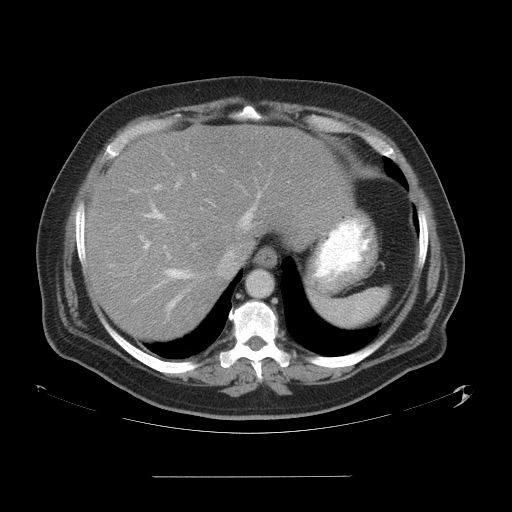
Contrast-enhanced abdominal CT, one axial slice; slice 44 of 58 in the series (ordered by position); 120 kVp; intravenous contrast given; soft-tissue window (W 400 / L 40 HU); 5 mm slice thickness; 512 × 512 image matrix, field of view 480 × 480 mm. Male patient, age 63 years. From the clinical record (not read from this slice): diagnosis: colorectal cancer liver metastases, imaged before liver resection; multiple liver metastases: no; largest metastasis: 4.2 cm; disease in both lobes: no.
Structures marked on this image (outlined manually by an expert reader):
- hepatic veins: bounding box <109,189,261,316> (left, top, right, bottom; pixels)
- liver: <85,126,347,340>
- planned liver remnant (the part of the liver to remain after resection): <85,198,225,340>
- portal vein (with intrahepatic branches): <140,174,196,249>